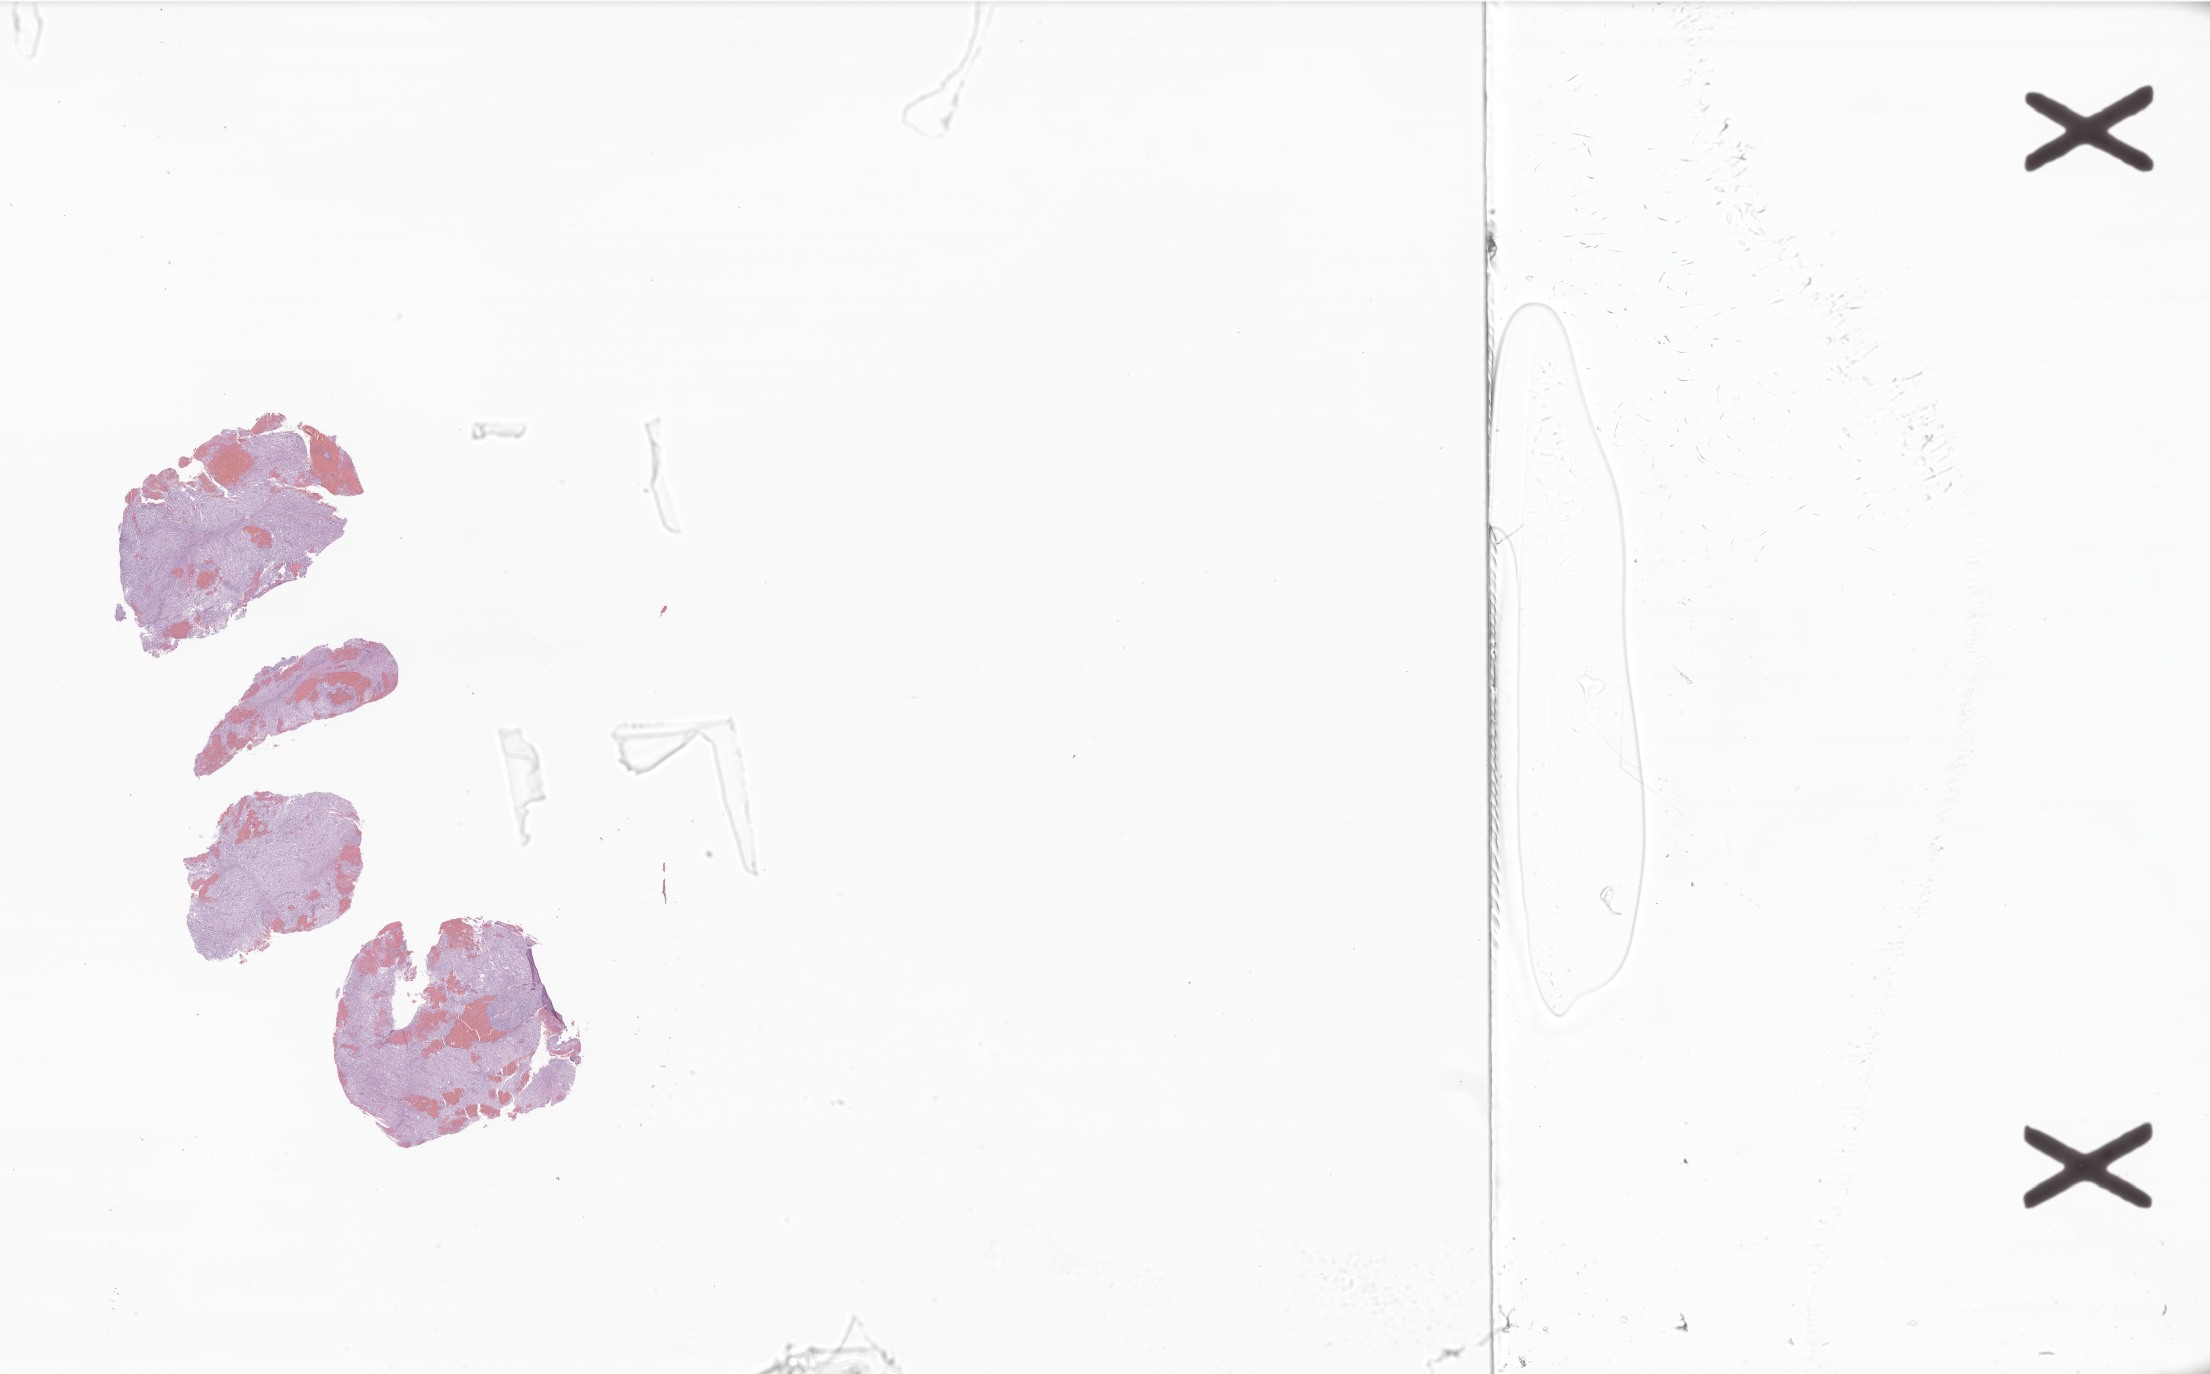
Digitized haematoxylin and eosin-stained section of tumor tissue from the spinal cord — shown as a low-resolution overview of the whole scanned area (about 37.3 x 23.2 mm), formalin-fixed, paraffin-embedded (FFPE) tissue. Patient male; age 217 months (18 years 1 month).
Diagnosis: Tumor cells, benign.